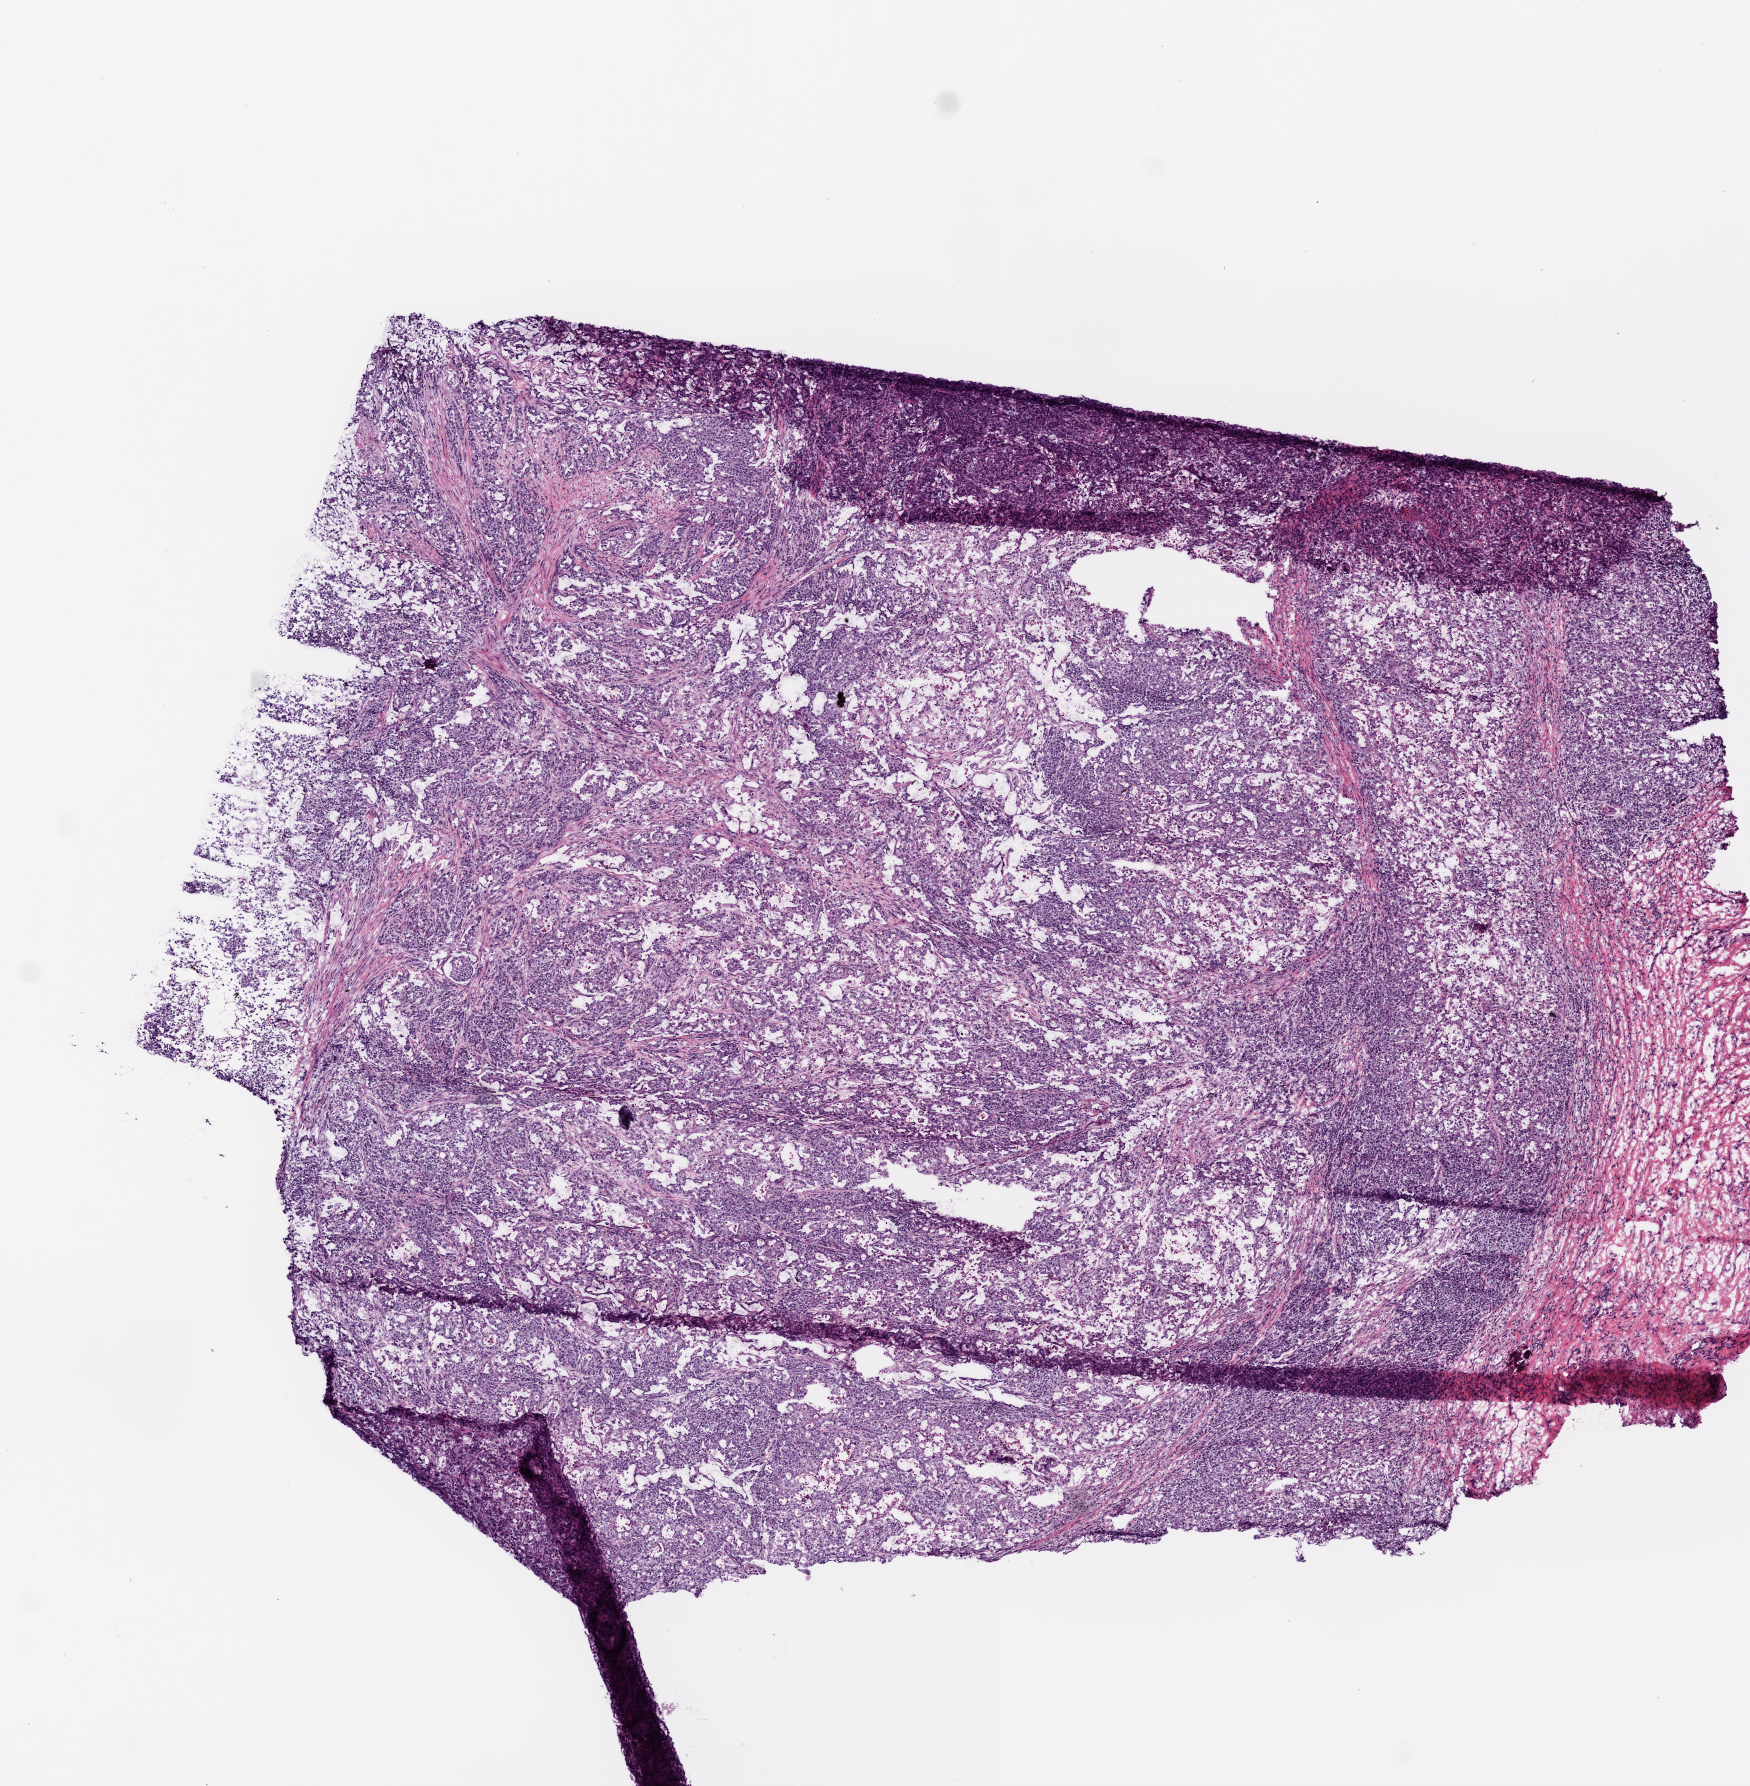
Whole-slide histology image, H&E — shown as a low-resolution overview of the whole scanned area (about 7.0 x 7.2 mm, acquisition: 20x scan). Frozen section. Sample: primary tumour, stomach. Female patient; age at initial diagnosis 69 years. Histologic grade: G3 (poorly differentiated). Composition of this section per pathologist review: tumour cells 80%, tumour nuclei 70%, normal cells 0%, stromal cells 10%, necrosis 10%.
Diagnosis: Carcinoma, diffuse type (gastric antrum). TNM: T4 N3 M1. AJCC pathologic stage: IV (6th edition). Lymph nodes positive (case pathology): 21 of 27 examined.